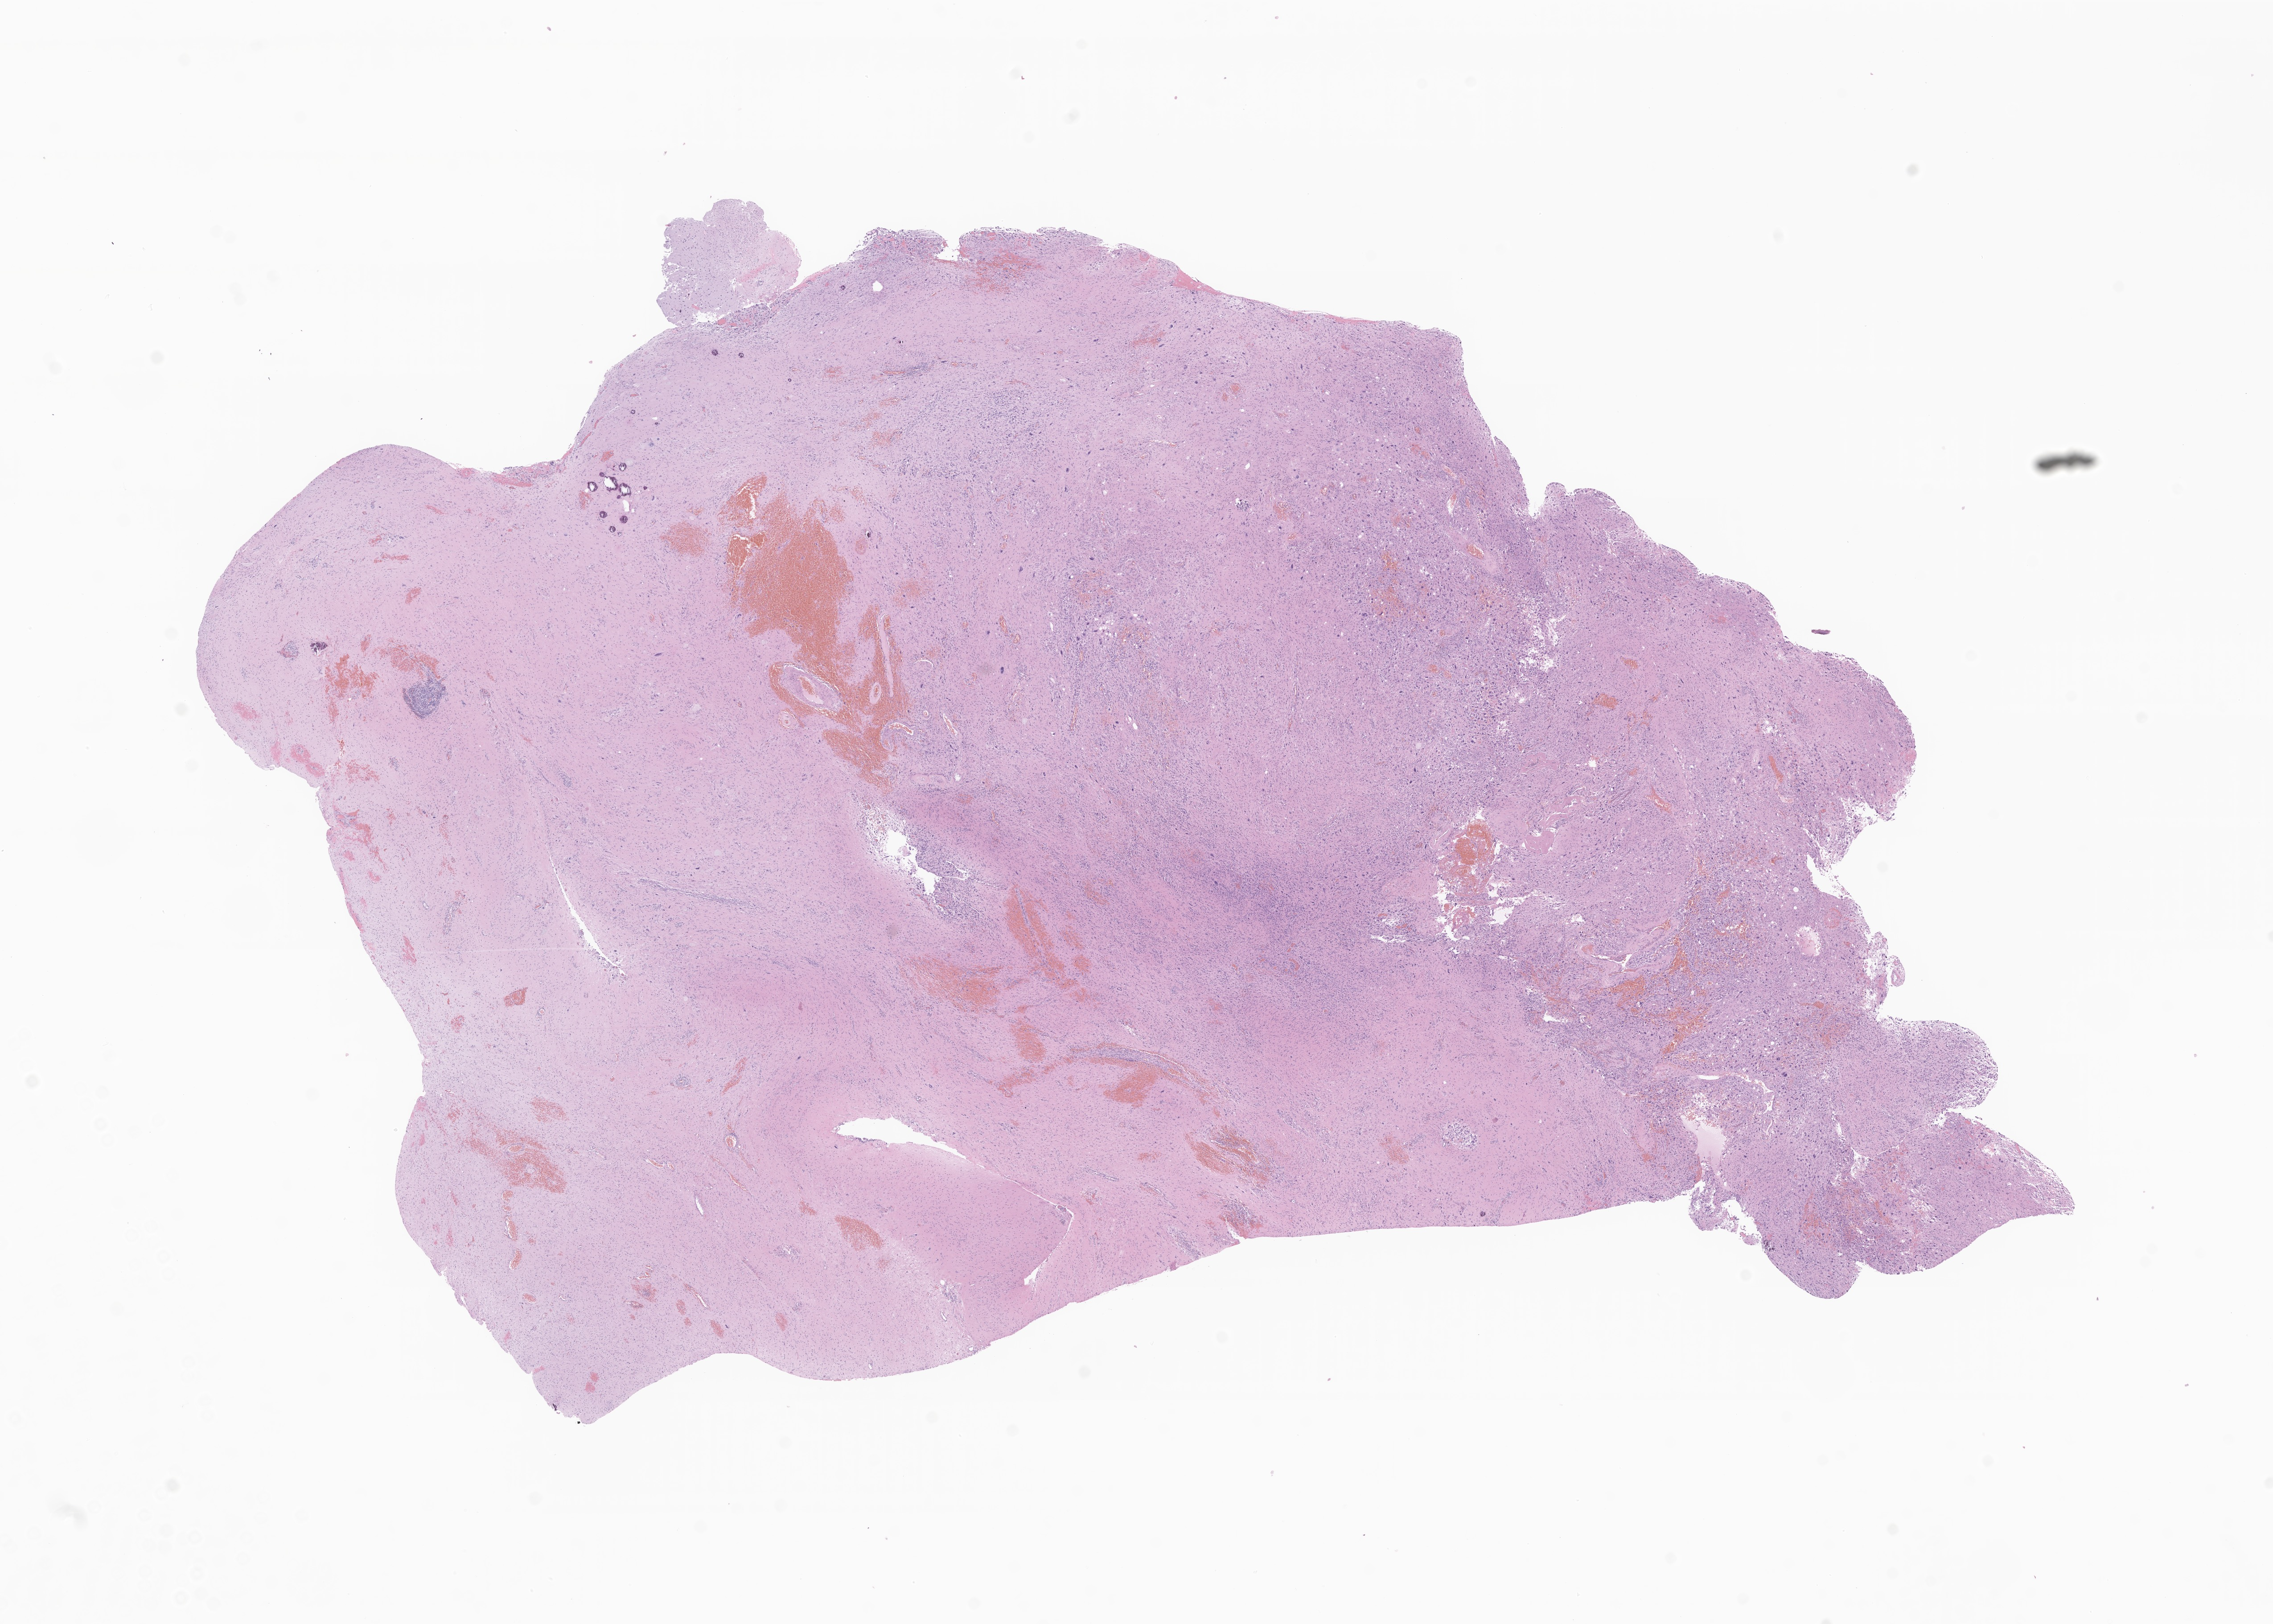
Whole-slide image, haematoxylin and eosin stain of tumor tissue from the brain, low-resolution overview of the scanned area, about 21.5 x 15.4 mm. Formalin-fixed paraffin-embedded section. Patient: male, age 177 months (14 years 9 months).
Diagnosis (ICD-O-3 morphology term): Glioma, malignant.